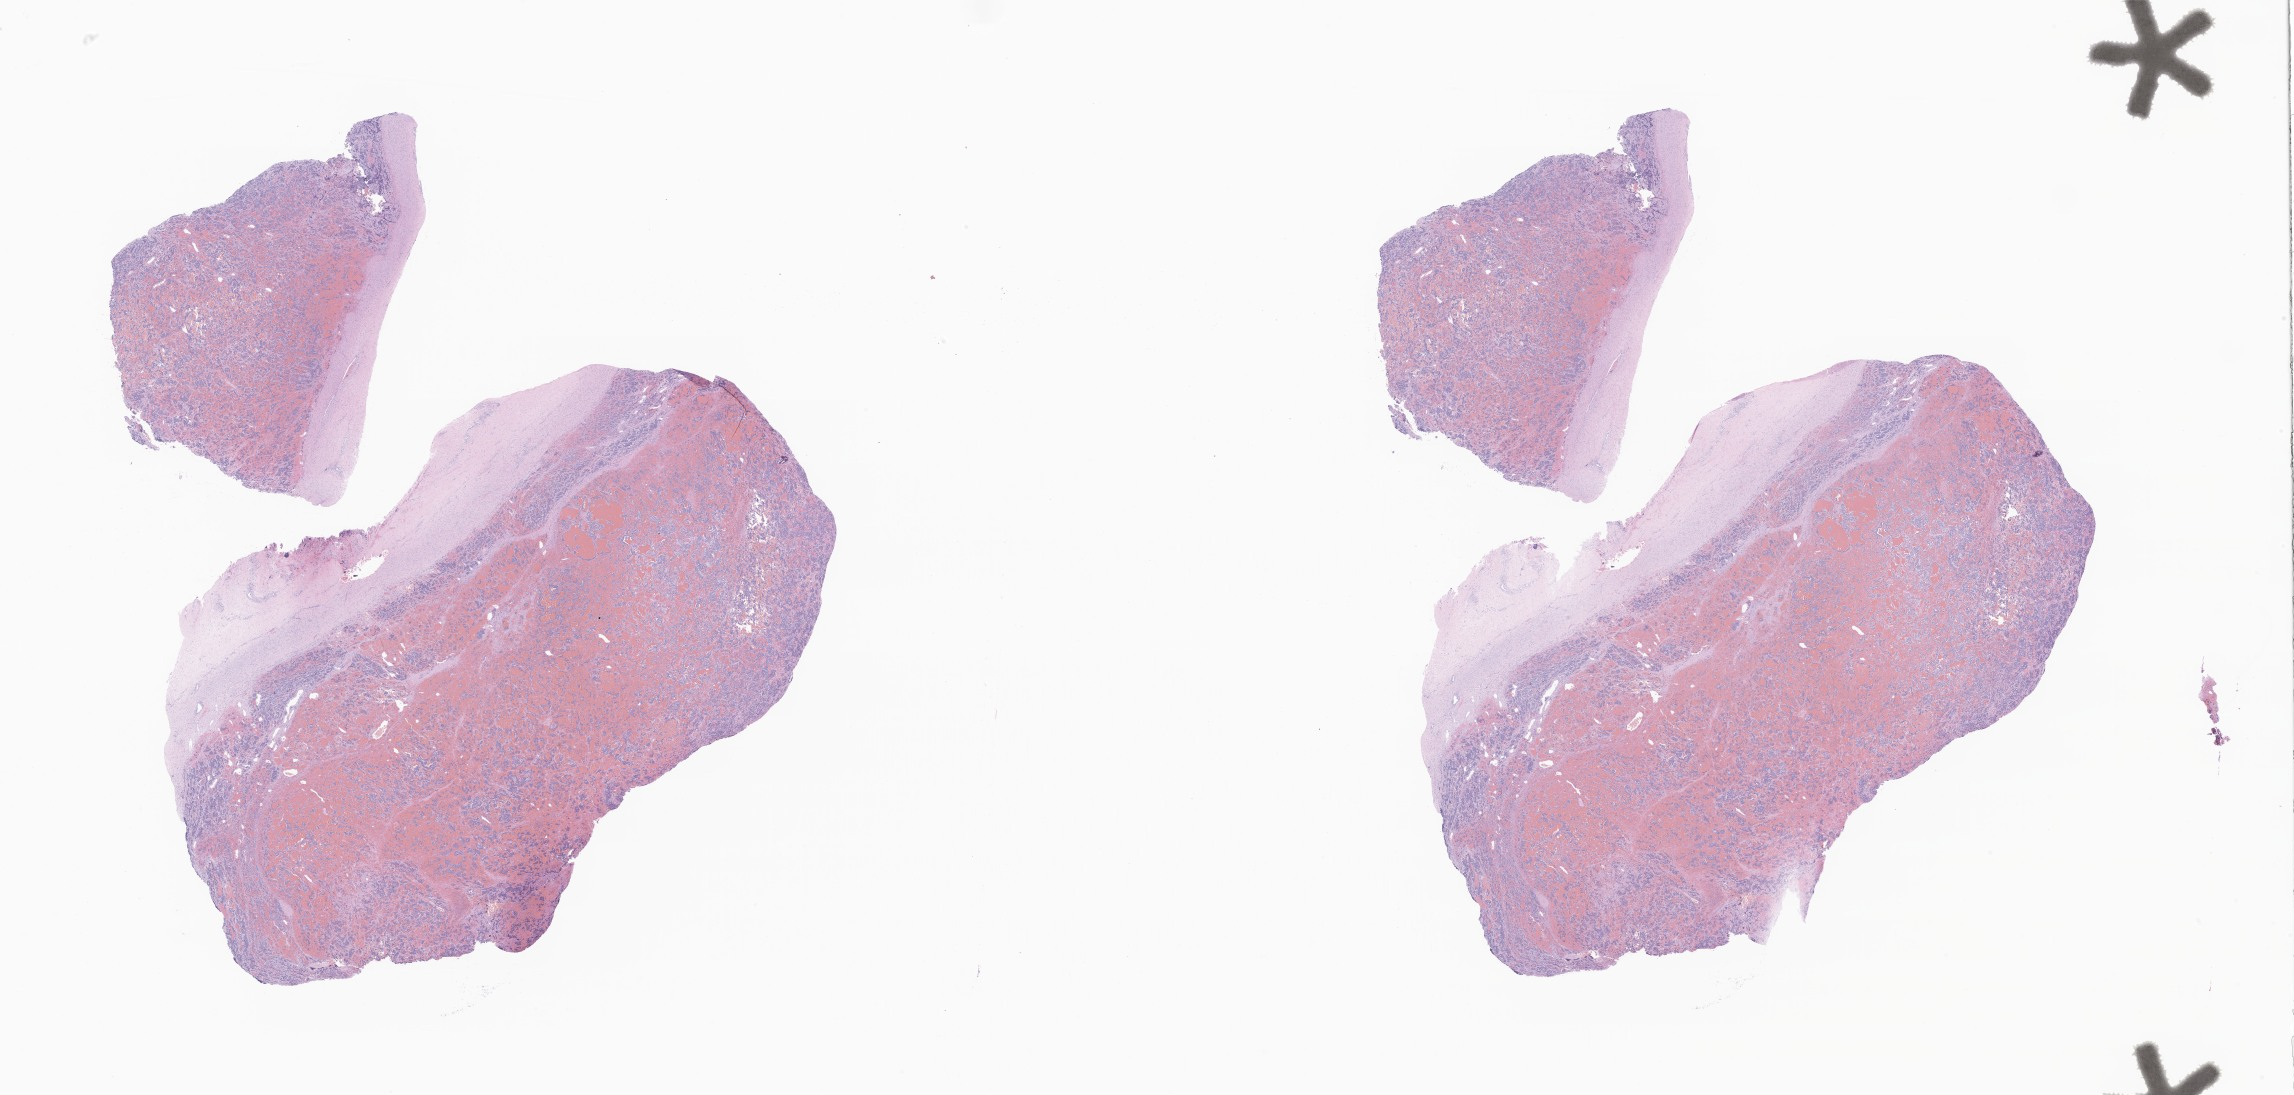
H&E whole-slide image of tumor tissue from the adrenal gland — low-resolution overview of the scanned area, about 38.7 x 18.5 mm; FFPE section. Patient: female, age 200 days.
Diagnosis (ICD-O-3 morphology term): Neuroblastoma, NOS.